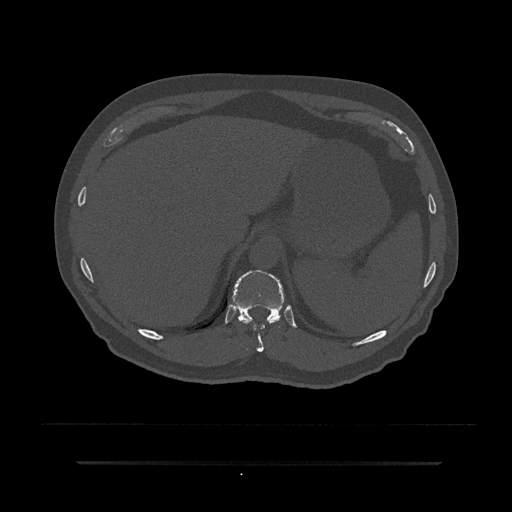
CT including the spine, one axial slice. Position 293 of 797 along the scan axis. Reconstruction kernel Br40s/3. 120 kVp. Bone window (W 1800 / L 400 HU). 0.5 mm slice thickness. 512 × 512 image matrix, field of view 464 × 464 mm. Male patient, age 59 years. Case-level facts recorded for this patient, not image findings: primary cancer: bile ducts; vertebrae with lytic lesions (as recorded): T10.
Annotated regions visible in this slice (semi-automatic segmentation, software-assisted and operator-edited):
- T10 vertebra: bounding box [x1, y1, x2, y2] px = [233, 288, 279, 352]
- T11 vertebra: [232, 270, 287, 323]